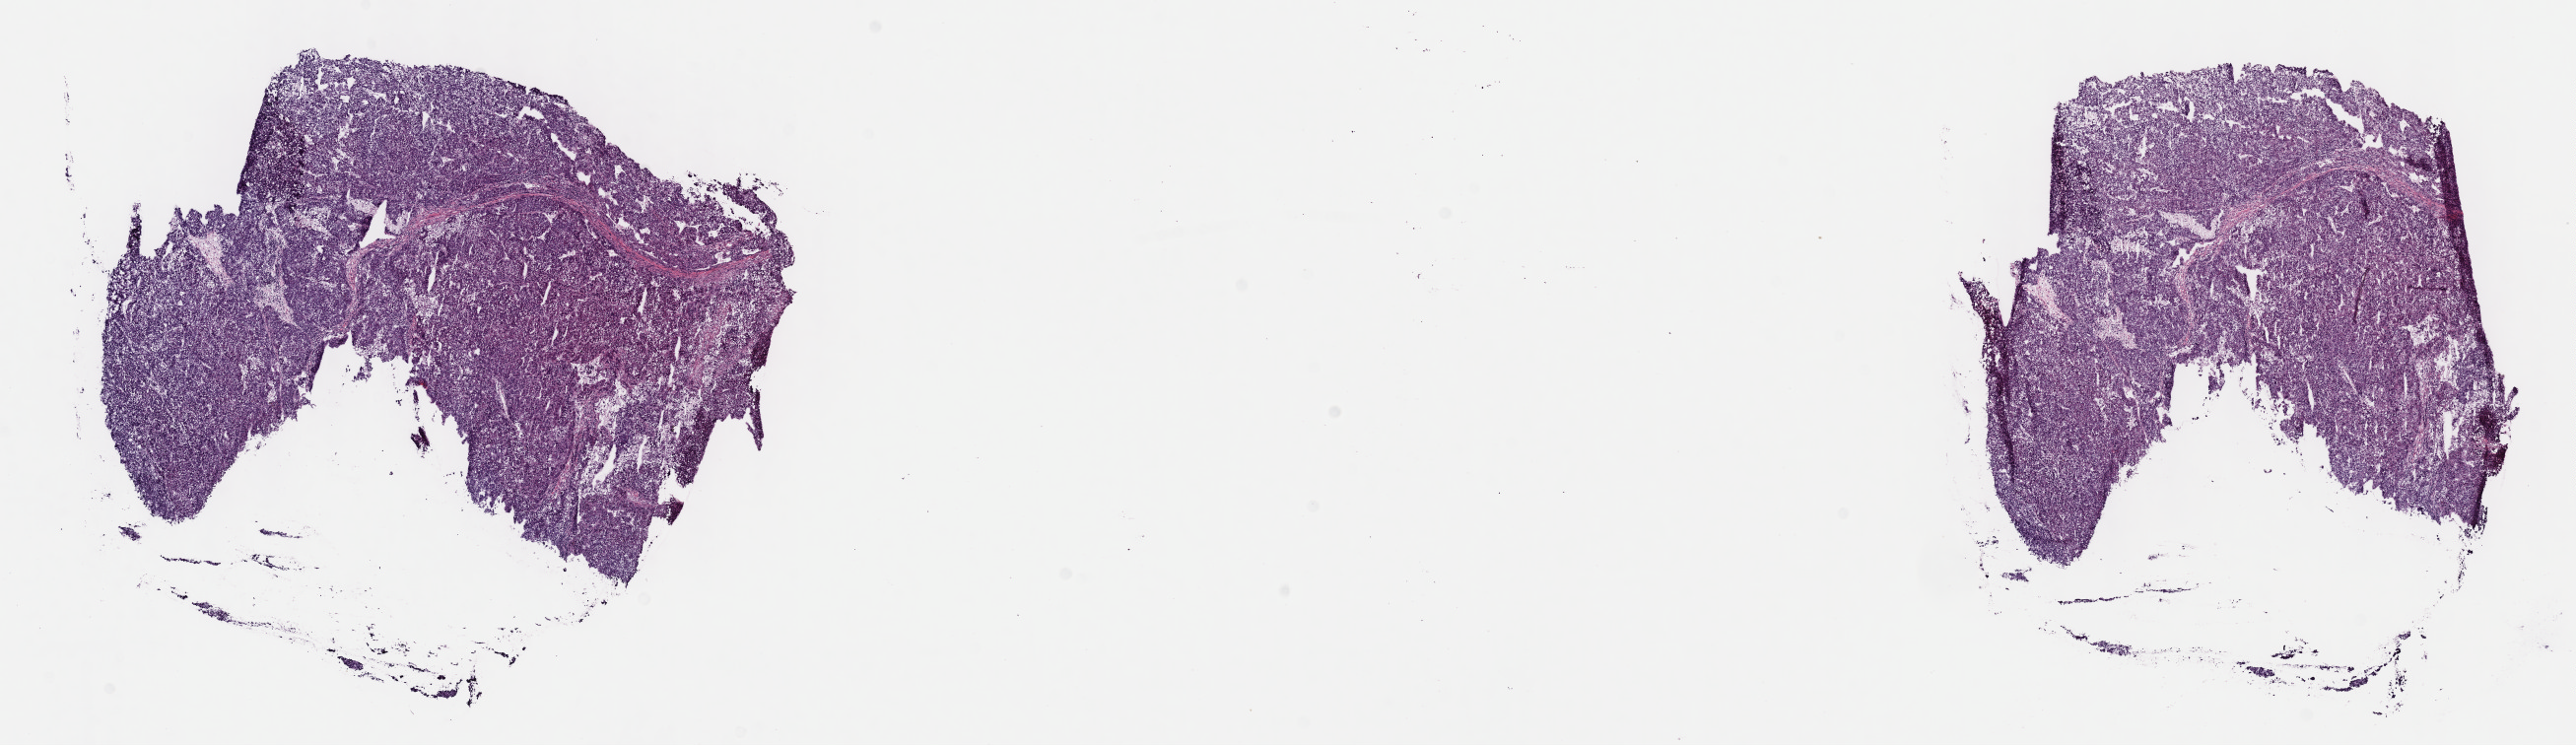
H&E-stained whole-slide image, whole scanned area (about 21.1 x 6.1 mm, slide scanned at 40x) shown as a low-resolution overview, frozen section from the top of the tissue portion, sample: primary tumour, liver. Female patient; age at initial diagnosis 74 years. Histologic grade: G3 (poorly differentiated). Slide review estimates, as recorded: tumour cells 85%, tumour nuclei 90%, normal cells 0%, stromal cells 10%, necrosis 5%. Inflammatory infiltration, as recorded: lymphocyte infiltration 7%, monocyte infiltration 1%, neutrophil infiltration 1%.
Histologic diagnosis: Hepatocellular carcinoma, NOS. AJCC pathologic stage: I.